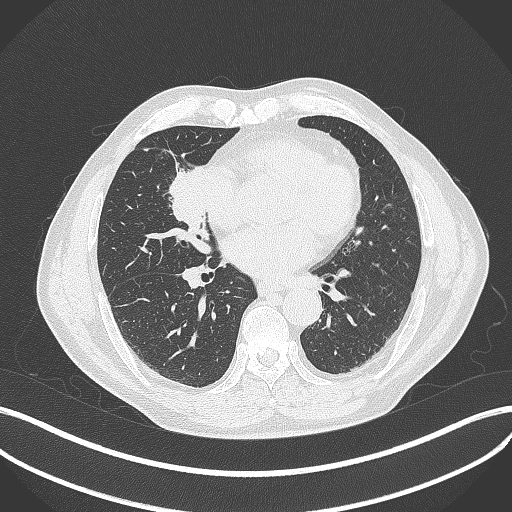
Chest CT, one axial slice; position 181 of 429 along the scan axis; reconstruction kernel B70f; 120 kVp; lung window (W 1500 / L -600 HU); 1 mm slice thickness; 512 × 512 image matrix, field of view 400 × 400 mm. Patient: male, 61 years. Case-level facts recorded for this patient, not image findings: clinical TNM (as recorded): T2b N1 M0.
Outlined on this slice (rectangle marked by the reading radiologist):
- lung tumour (recorded histology: squamous cell carcinoma): bounding box [x1, y1, x2, y2] px = [166, 162, 215, 239]